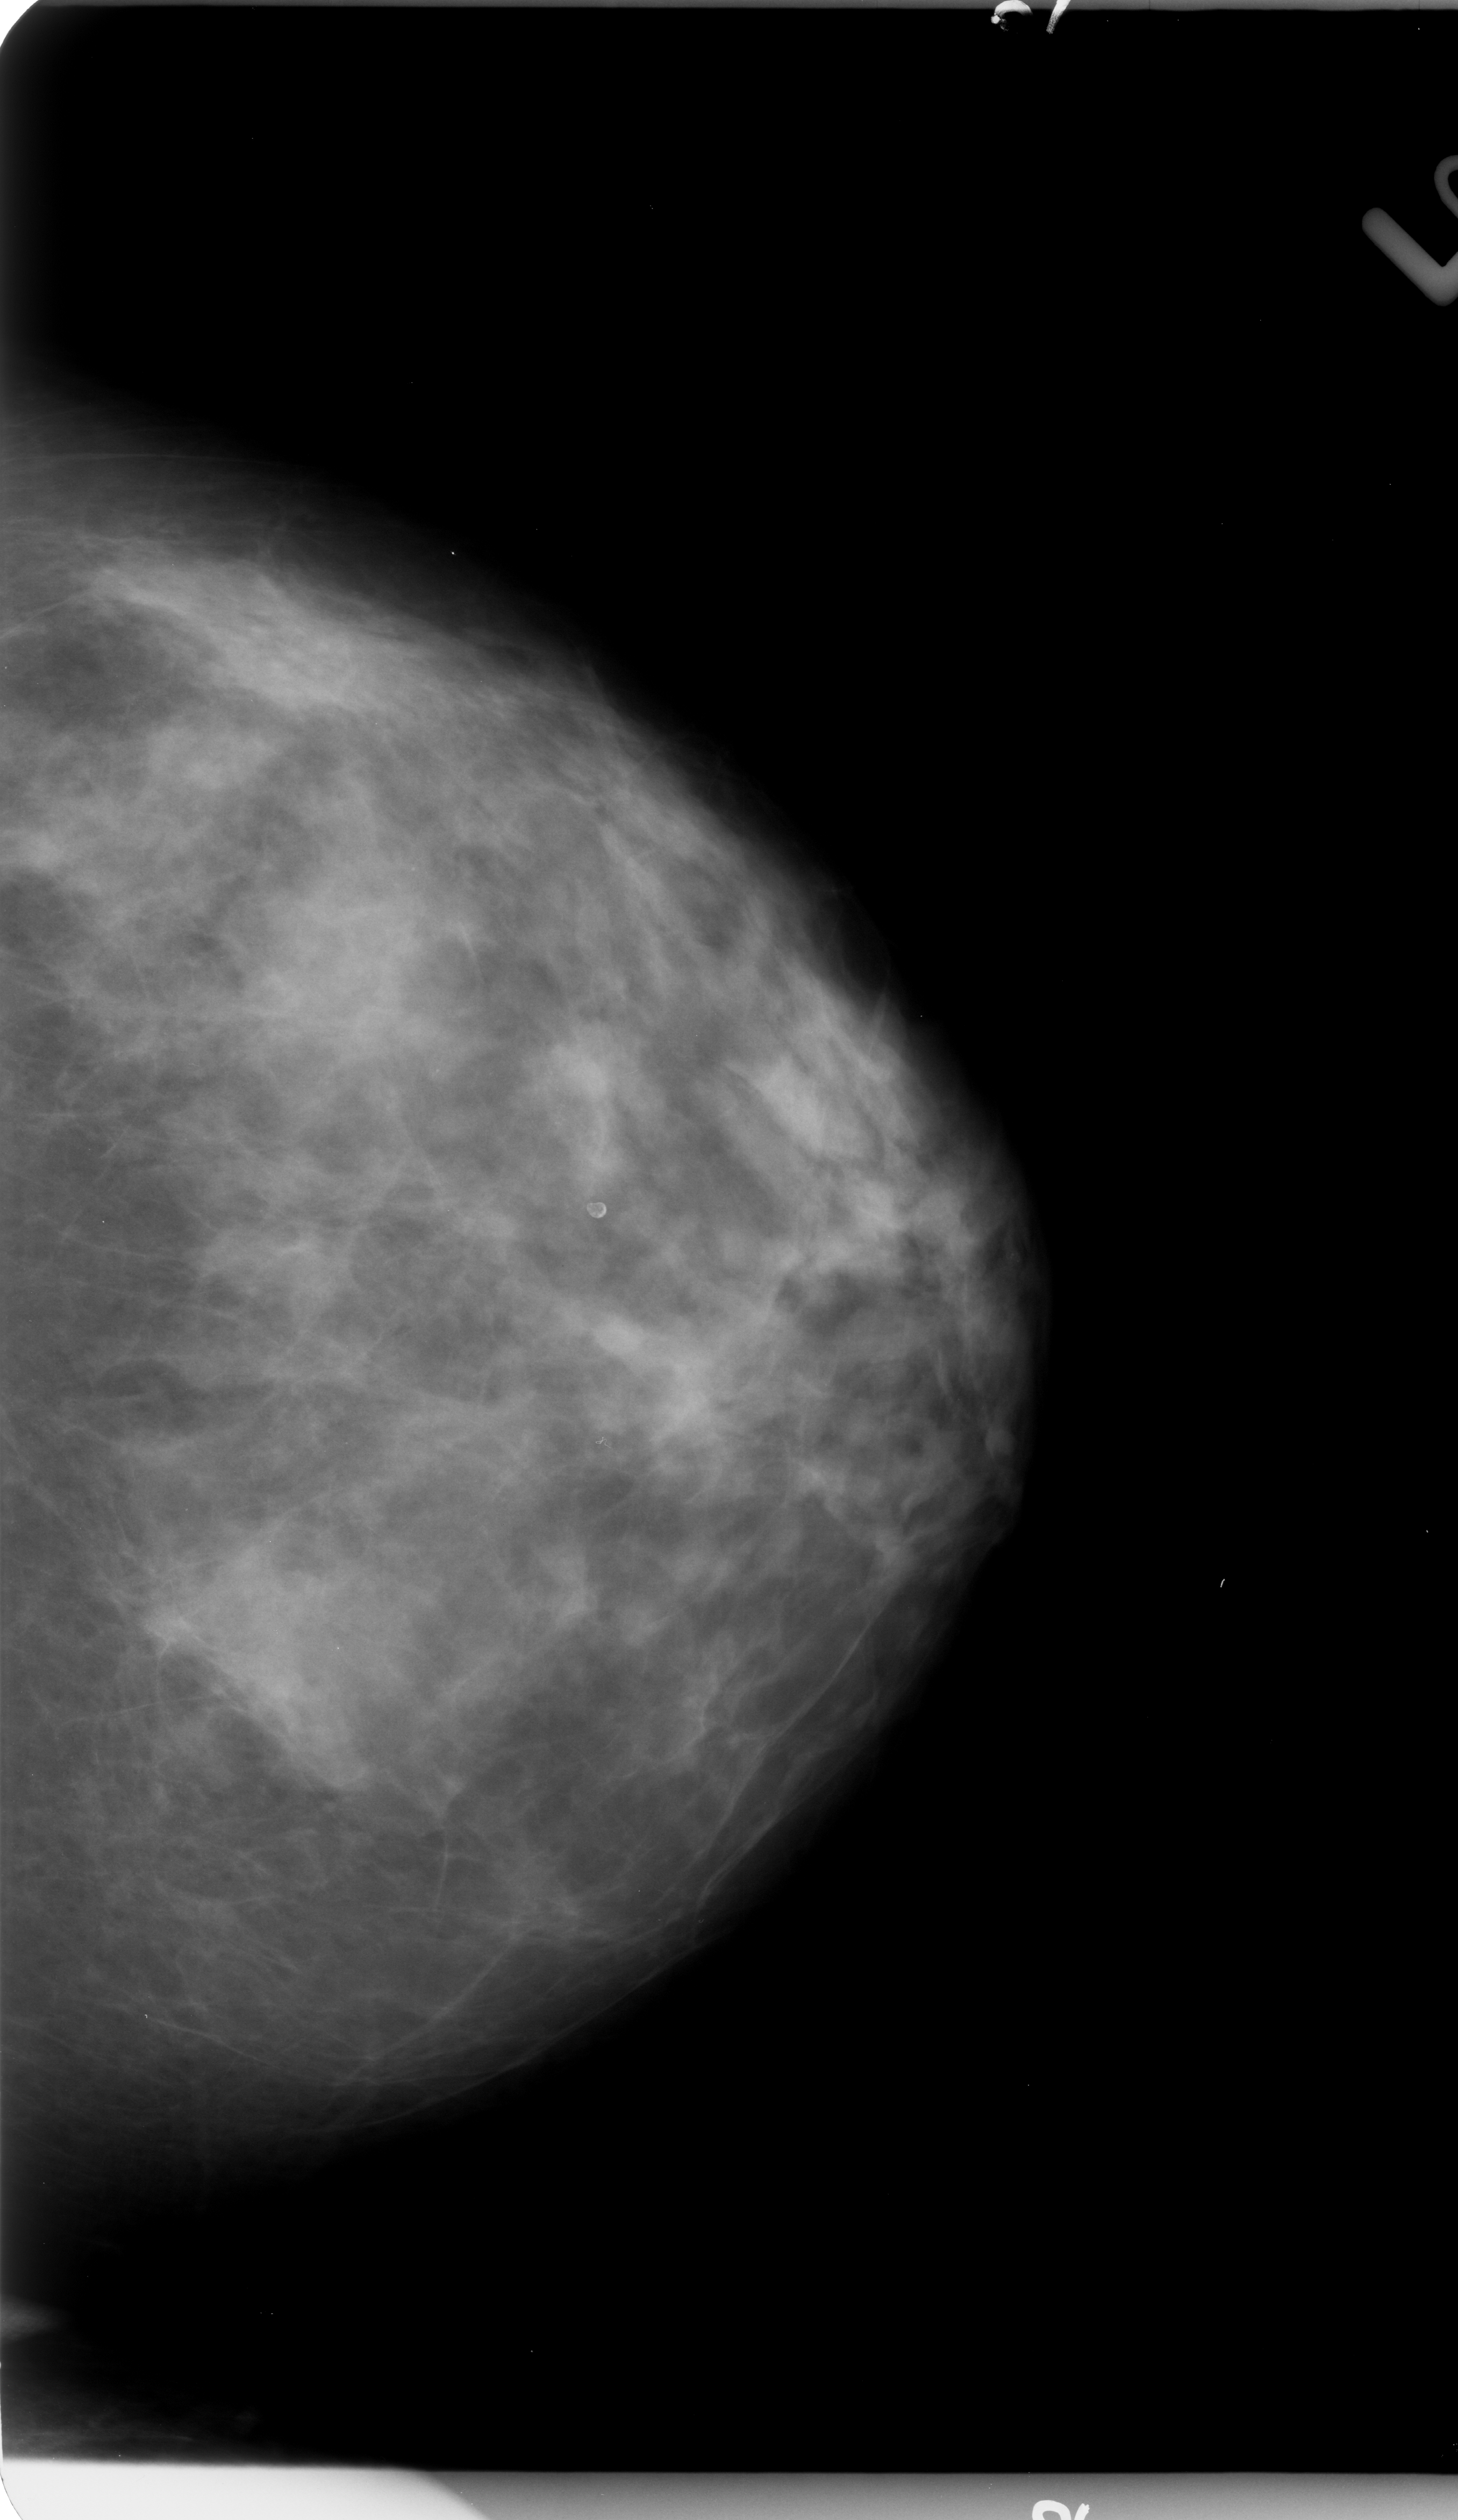
Digitized screen-film mammogram. Left breast. CC view. 1458 × 2520 image matrix.
Expert-marked regions of interest on this film, with their recorded descriptors:
- calcifications, morphology punctate, distribution clustered; BI-RADS assessment category 3; pathology (as recorded): benign: bounding box (x1, y1, x2, y2) in pixels: (481, 989, 685, 1287)